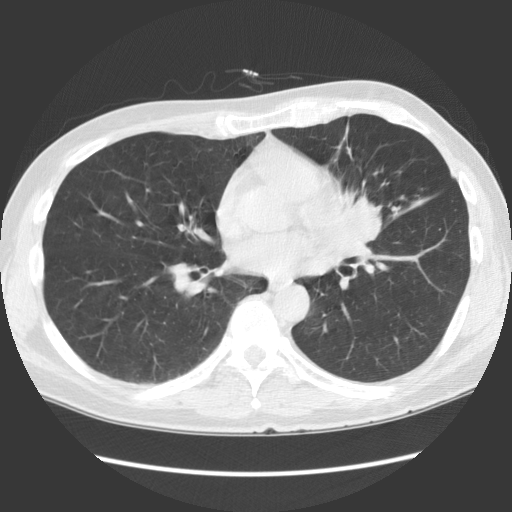
Axial slice from a low-dose chest CT screening exam; first (baseline) screen; lung window (W 1500 / L -600 HU); 140 kVp; 512 × 512 image matrix. Male participant, aged 61 years at enrolment. Former smoker at enrolment.
Expert-annotated lung lesion, bounding box [x1, y1, x2, y2] px = [308, 180, 402, 279]. Screening reader's record for this exam (one nodule recorded; not confirmed to be the boxed lesion): non-calcified nodule or mass ≥4 mm, lingula, 35 × 35 mm, spiculated (stellate) margins, soft tissue attenuation. Official screen result: positive, change unspecified: nodule(s) >= 4 mm or enlarging nodule(s), mass(es), or other non-specific abnormalities suspicious for lung cancer. Later outcome: lung cancer diagnosed 58 days after this screen — squamous cell carcinoma, NOS, left hilum, left main stem bronchus, poorly differentiated (G3), stage IA (AJCC 6th edition), 40 mm at pathology.